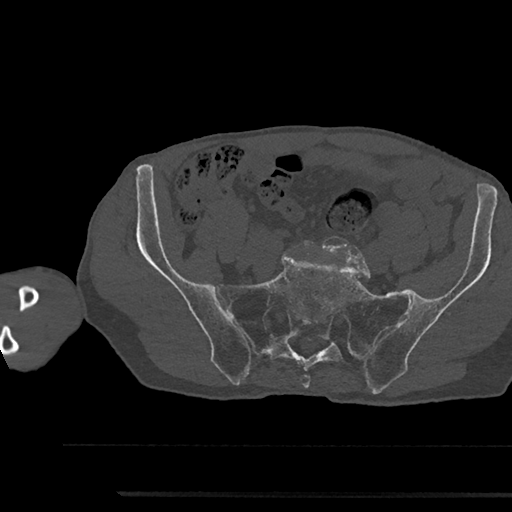
CT including the spine, one axial slice. 120 kVp. Bone window (W 1800 / L 400 HU). 0.5 mm slice thickness. 512 × 512 image matrix, field of view 367 × 367 mm. Patient: male, 79 years. Case-level facts recorded for this patient, not image findings: primary cancer: prostate.
Structures marked on this image (semi-automatically segmented with operator editing):
- L5 vertebra: bounding box <293,240,315,248> (left, top, right, bottom; pixels)